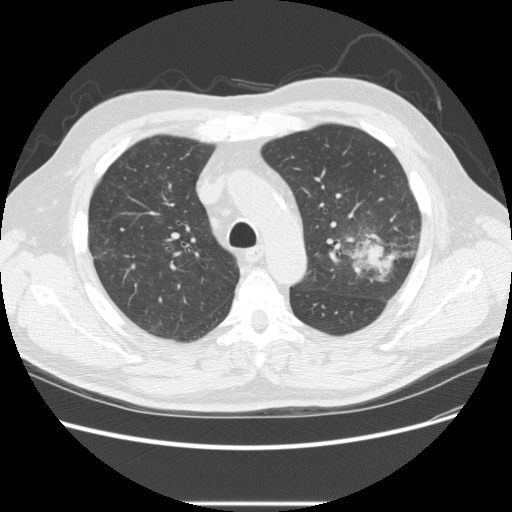
Low-dose screening chest CT, one axial slice. Position 165 of 233 along the scan axis. Reconstruction kernel STANDARD. Lung window (W 1500 / L -600 HU). 2.5 mm slice thickness. 512 × 512 image matrix.
Outlined on this slice (outlined manually by an expert reader):
- lesion 1 (tumor, upper lobe of left lung): bounding box (x1, y1, x2, y2) in pixels: (352, 235, 394, 283)